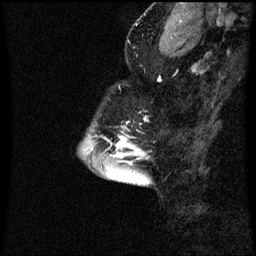
Breast MRI (dynamic contrast-enhanced), one sagittal slice; position 19 of 60 along the scan axis; dynamic contrast-enhanced series, image 2 of 3 at this slice position (ordered by acquisition); 1.5 T; TE 4.2 ms, TR 8.9 ms; 2 mm slice thickness; 256 × 256 image matrix, field of view 200 × 200 mm. Female patient, age 43 years. Case-level facts recorded for this patient, not image findings: setting: breast cancer imaged before/during neoadjuvant chemotherapy; receptor status: HR-positive, HER2-negative.
Outlined on this slice (semi-automatically segmented with operator editing):
- analysis volume of interest (the breast-tissue region the enhancement analysis was run in; not a lesion): bounding box [x1, y1, x2, y2] px = [96, 118, 147, 159]
- tumour enhancement mask (voxels above the 70 % enhancement threshold inside the analysis volume of interest): [118, 118, 147, 155]